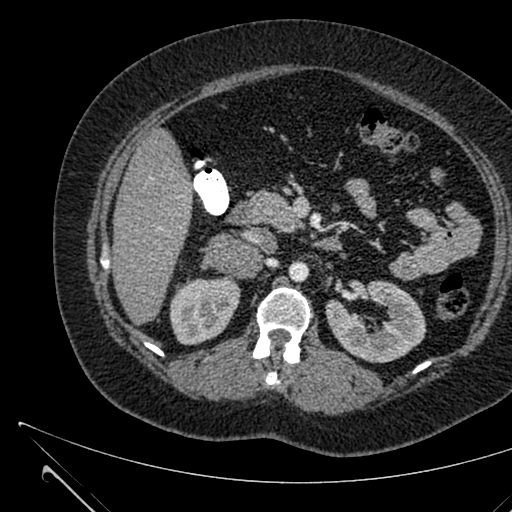
Contrast-enhanced abdominal CT, one axial slice. Position 358 of 731 along the scan axis. 120 kVp. Intravenous contrast given. Soft-tissue window (W 400 / L 40 HU). 512 × 512 image matrix, field of view 376 × 376 mm. Patient: female, 36 years. Case-level facts recorded for this patient, not image findings: diagnosis: adrenocortical carcinoma; tumour side: right adrenal.
Annotated regions visible in this slice (semi-automatic segmentation, software-assisted and operator-edited):
- mass: bounding box <211,235,259,278> (left, top, right, bottom; pixels)